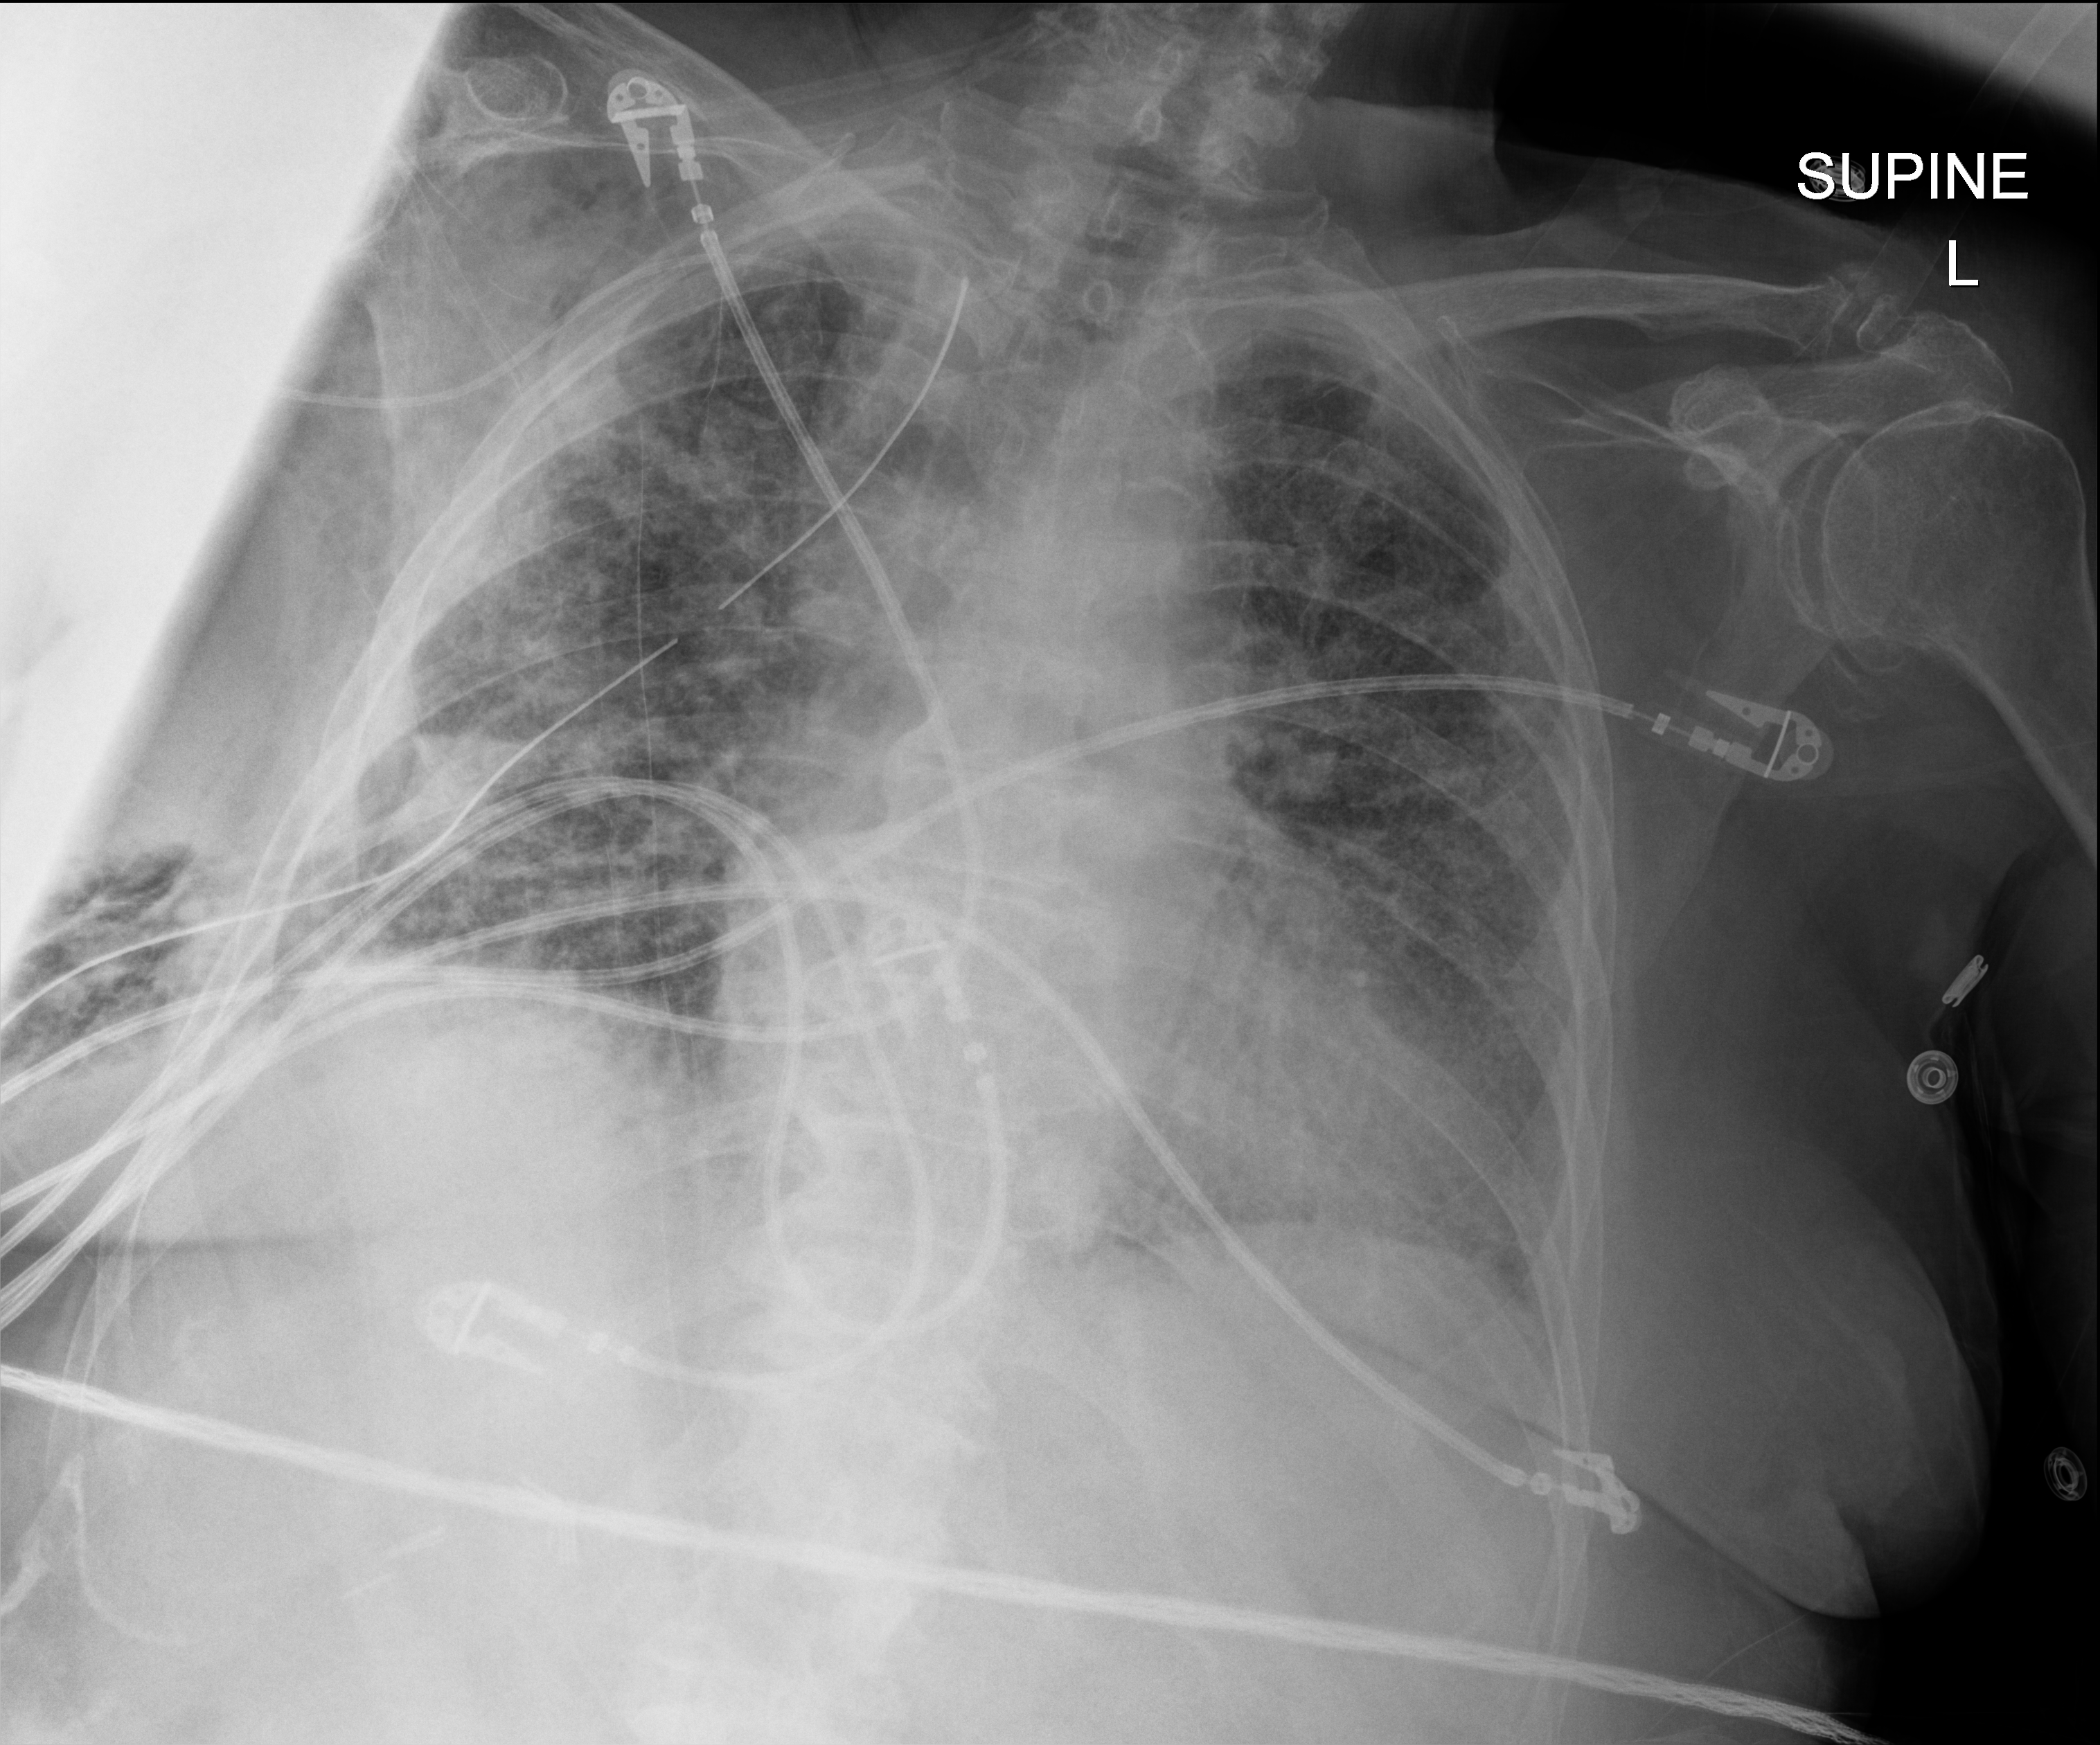
Chest radiograph; anteroposterior (AP) projection. Patient hospitalised with COVID-19; female, aged 75–90 years.
Hospital-stay facts (about this admission, not read from this image; timing relative to this image not recorded): mechanically ventilated during this hospital stay: yes.